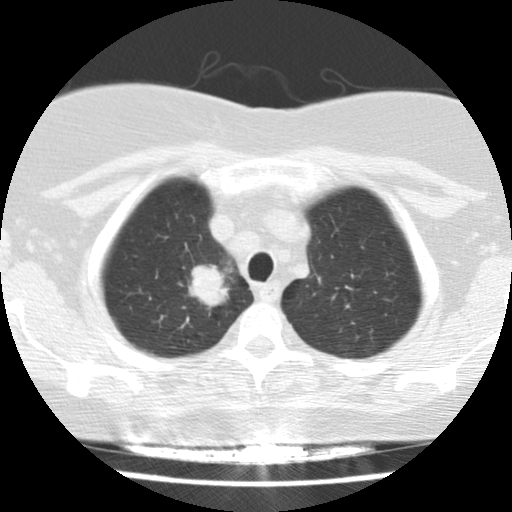
Chest CT (low-dose screening protocol), one axial image; baseline screening round; lung window (W 1500 / L -600 HU); 2.5 mm slice thickness; standard (soft-tissue) reconstruction kernel (STANDARD). Female participant, aged 58 years at enrolment. Former smoker at enrolment.
Lesion marked by an expert reader, bounding box [x1, y1, x2, y2] px = [169, 245, 247, 323]. Reader record for this screening exam (exam-level; its link to the box is not recorded): non-calcified nodule or mass ≥4 mm, right upper lobe, 28 × 24 mm, spiculated (stellate) margins, soft tissue attenuation. Participant outcome: lung cancer diagnosed 40 days after this screen — adenocarcinoma, NOS, right upper lobe, poorly differentiated (G3), stage IB (AJCC 6th edition), 29 mm at pathology.